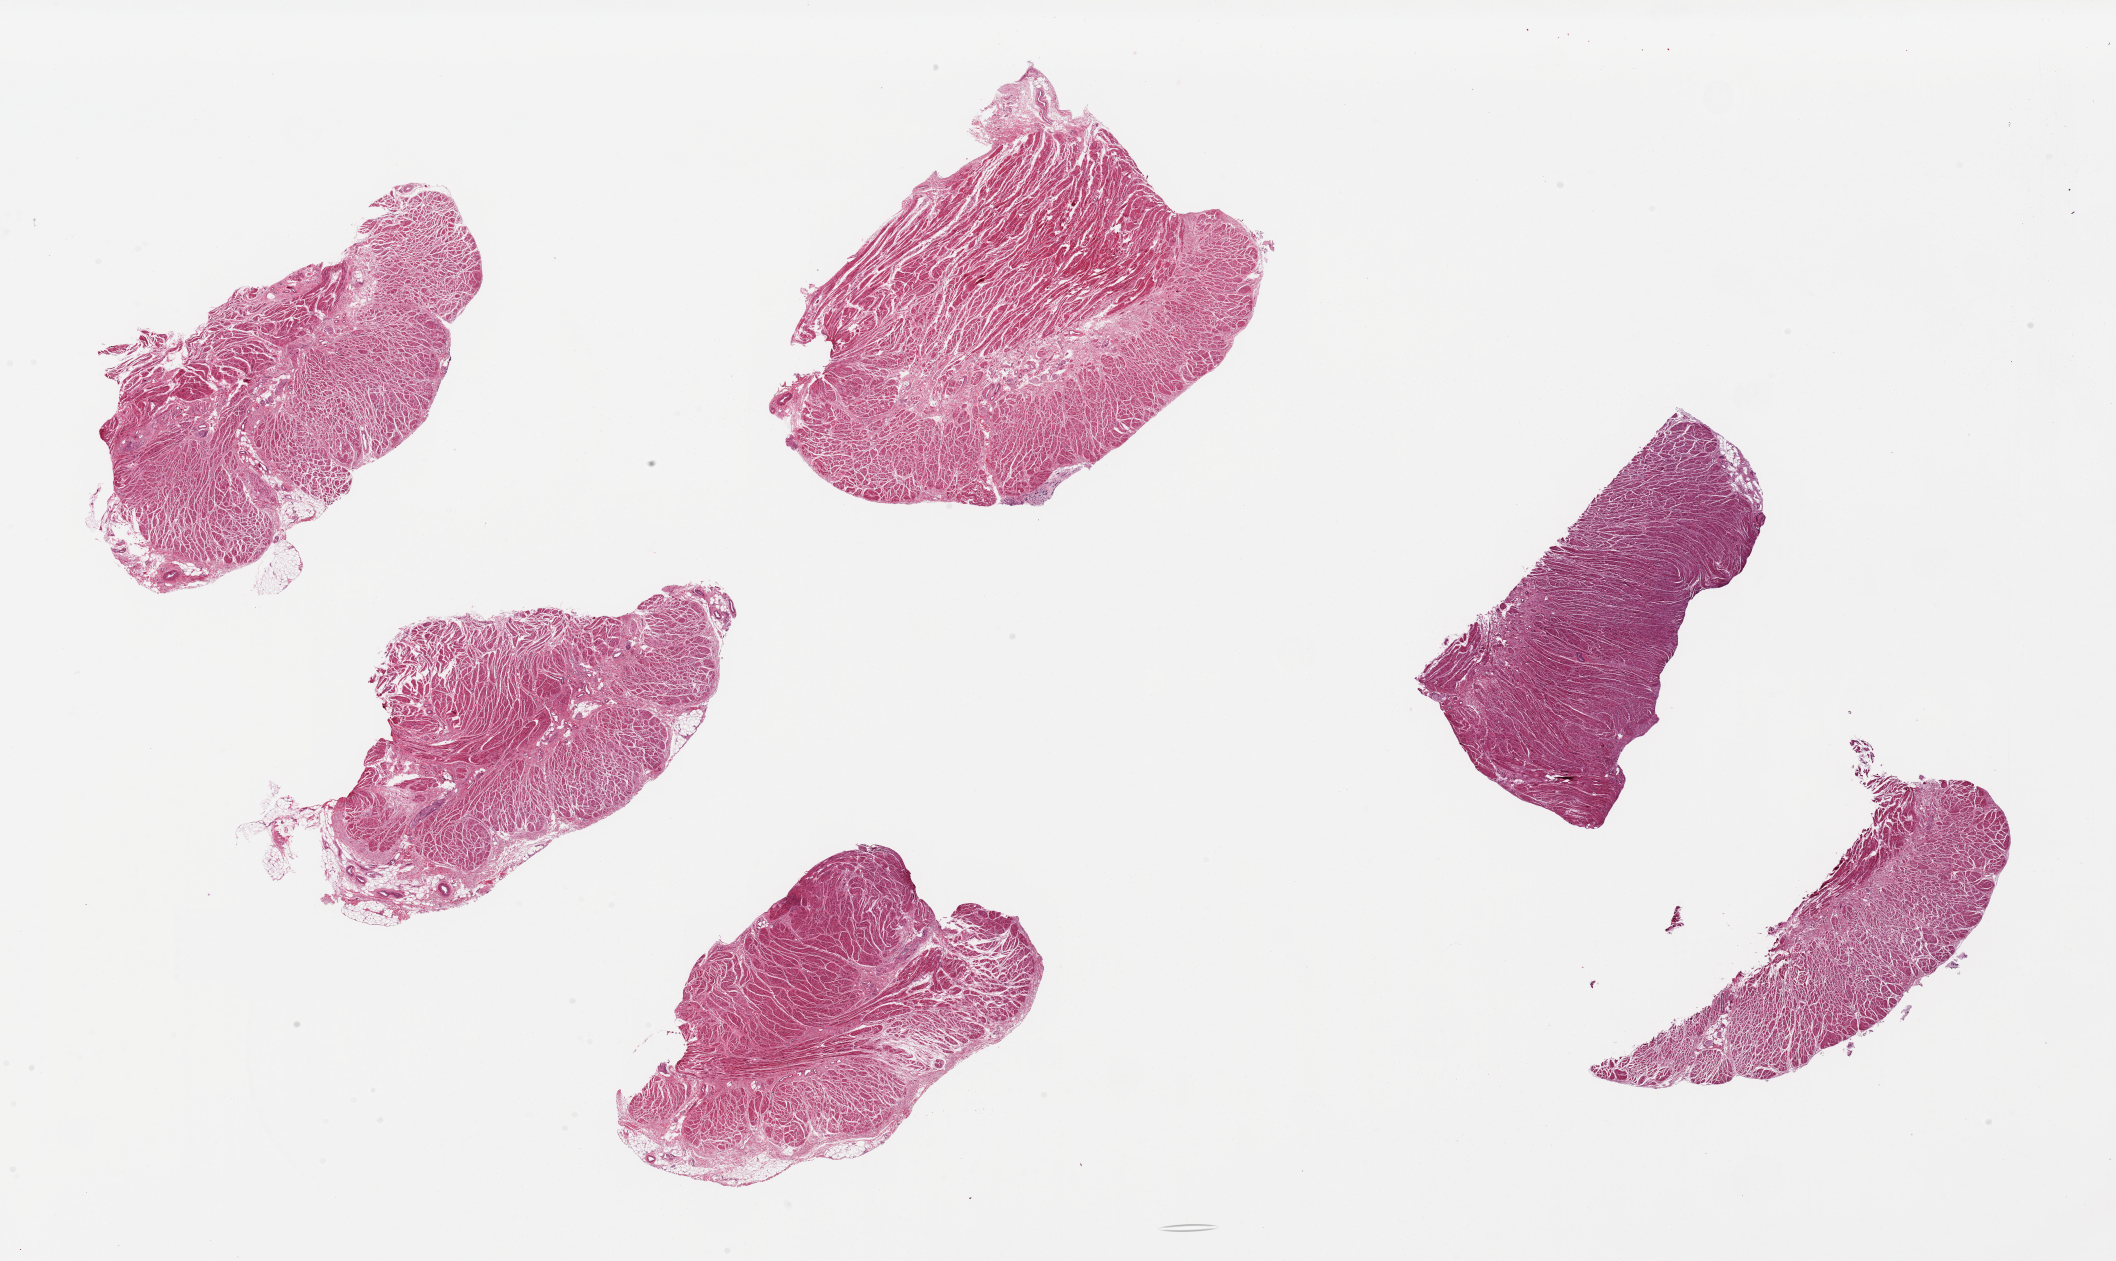
Whole-slide image, H&E stain — low-resolution overview of the scanned area, about 33.5 x 19.9 mm. PAXgene-fixed, paraffin-embedded tissue. Section of esophageal muscle (target tissue). Donor tissue sample.
* pathologist's review note for this sample: 6 ~6.5x4mm pieces